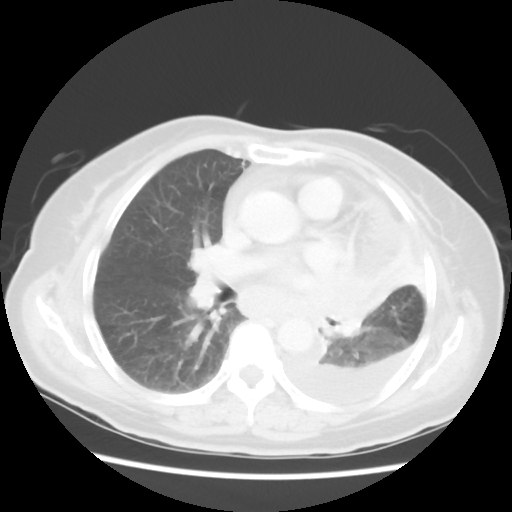
Chest CT, one axial slice; slice 30 of 52 in the series (ordered by position); 120 kVp; lung window (W 1500 / L -600 HU); 5 mm slice thickness; 512 × 512 image matrix, field of view 336 × 336 mm. Patient: female, 72 years. Case-level facts recorded for this patient, not image findings: clinical TNM (as recorded): T4 N3 M1b; histopathological grade: G3.
Structures marked on this image (bounding box drawn by a radiologist):
- lung tumour (recorded histology: large cell carcinoma): bounding box [x1, y1, x2, y2] px = [307, 265, 378, 350]